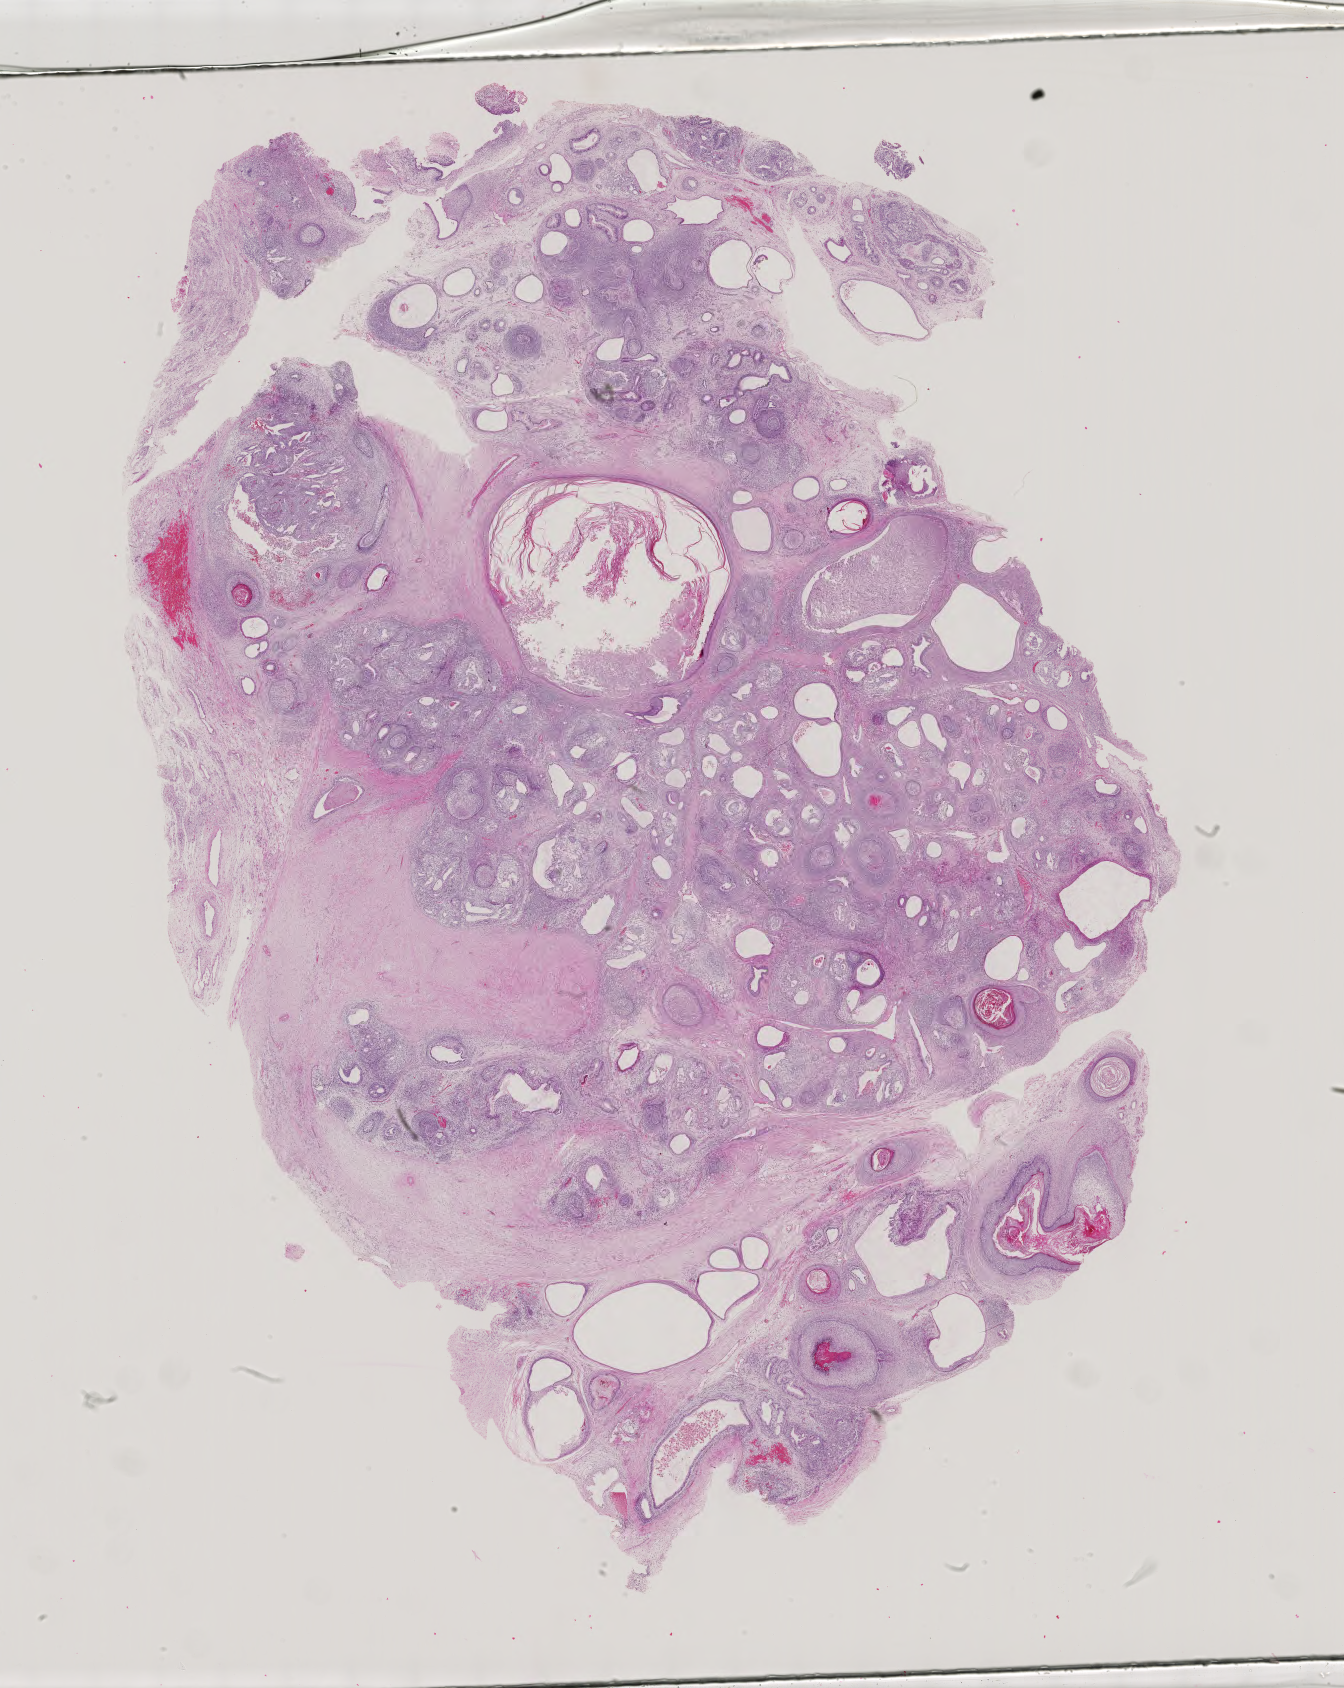
Whole-slide histology image, H&E, a low-resolution overview of the entire scanned area, about 19.6 x 24.6 mm (acquisition: 40x scan). Male patient.
* specimen: formalin-fixed paraffin-embedded (FFPE) diagnostic section; sample: primary tumour, testis